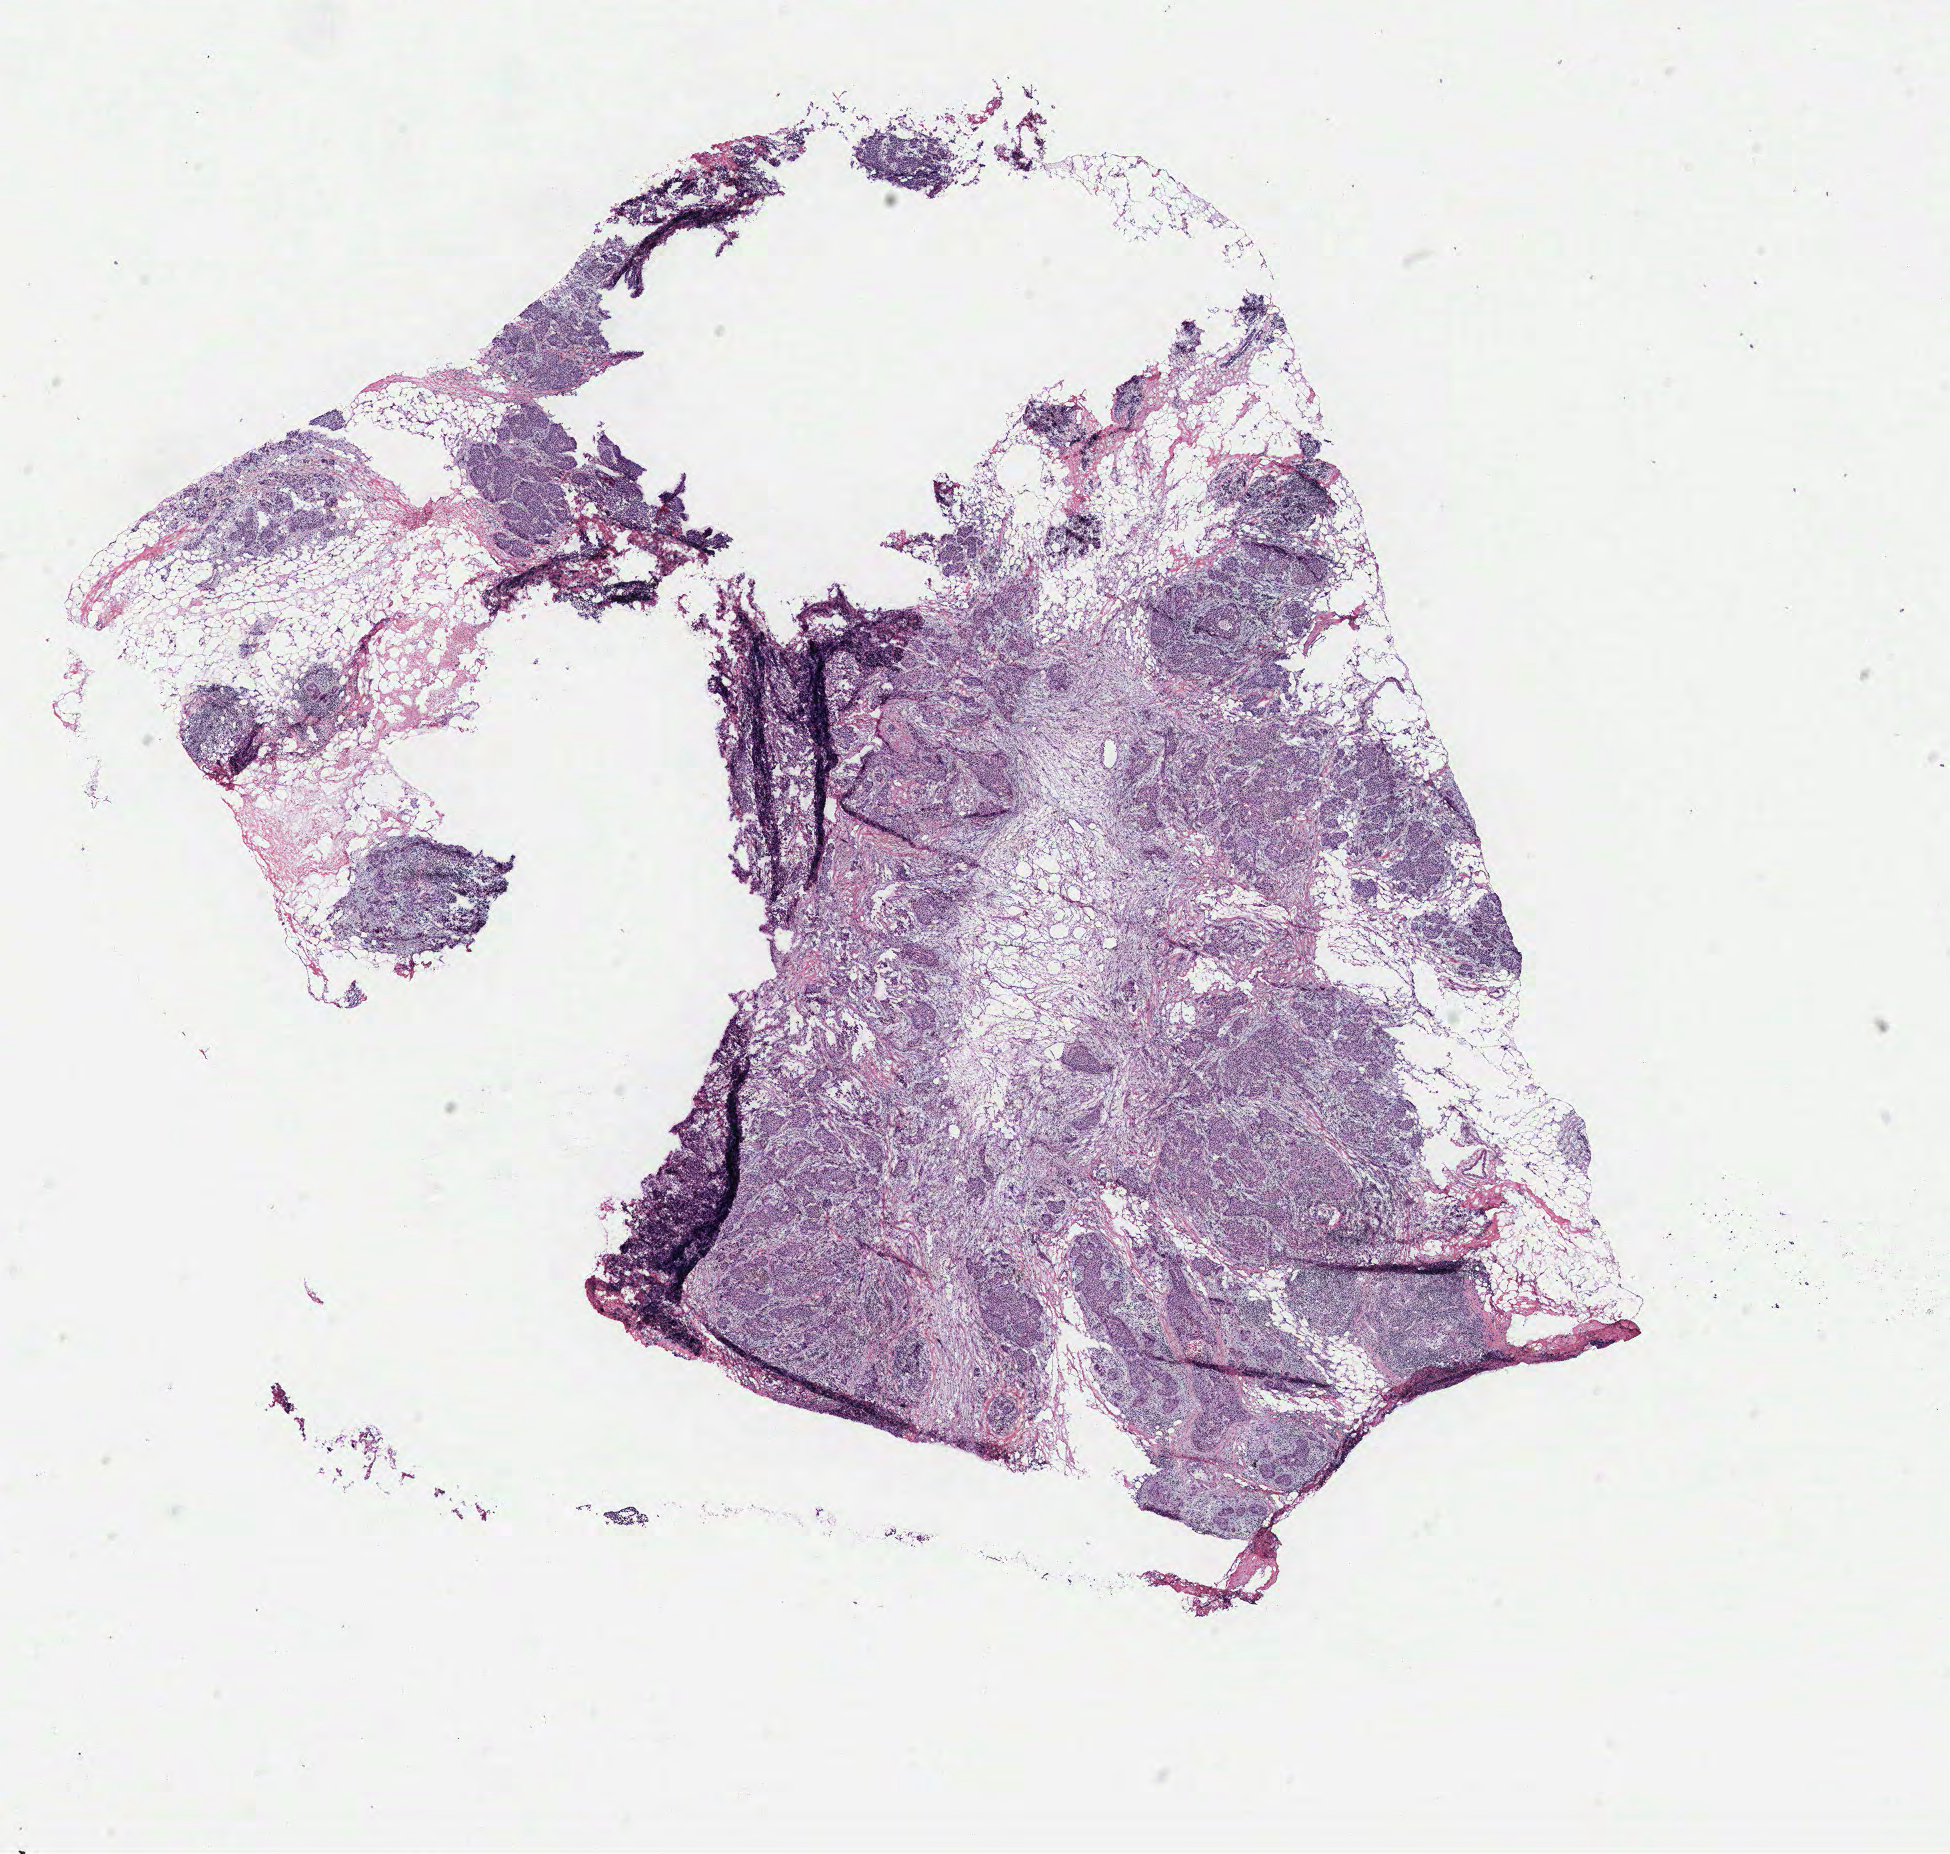
Digitized H&E tissue section (whole slide), low-resolution overview of the scanned area, about 15.6 x 14.8 mm, breast, tissue type not recorded. Patient: female, age 37 years.
Patient diagnosis: Infiltrating duct carcinoma, NOS.